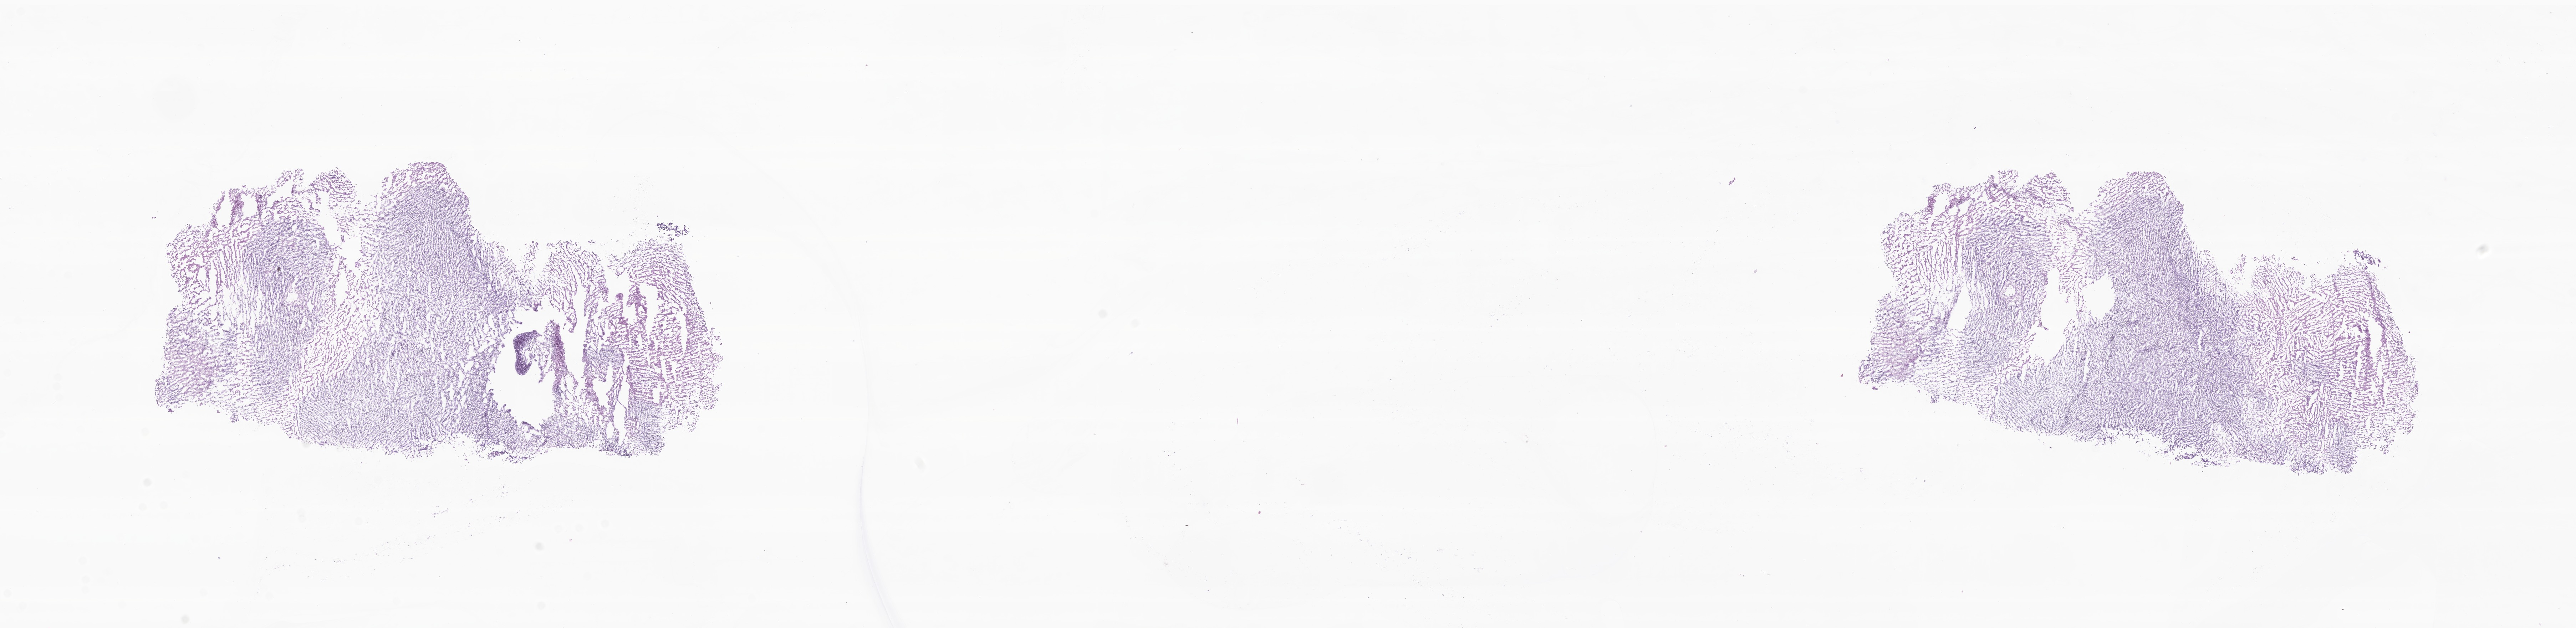
Digitized H&E-stained section of tumor tissue from the brain — low-resolution overview of the scanned area, about 30.5 x 7.4 mm, frozen section. Patient male; age 47 months (3 years 11 months).
Diagnosis: Atypical teratoid/rhabdoid tumor.